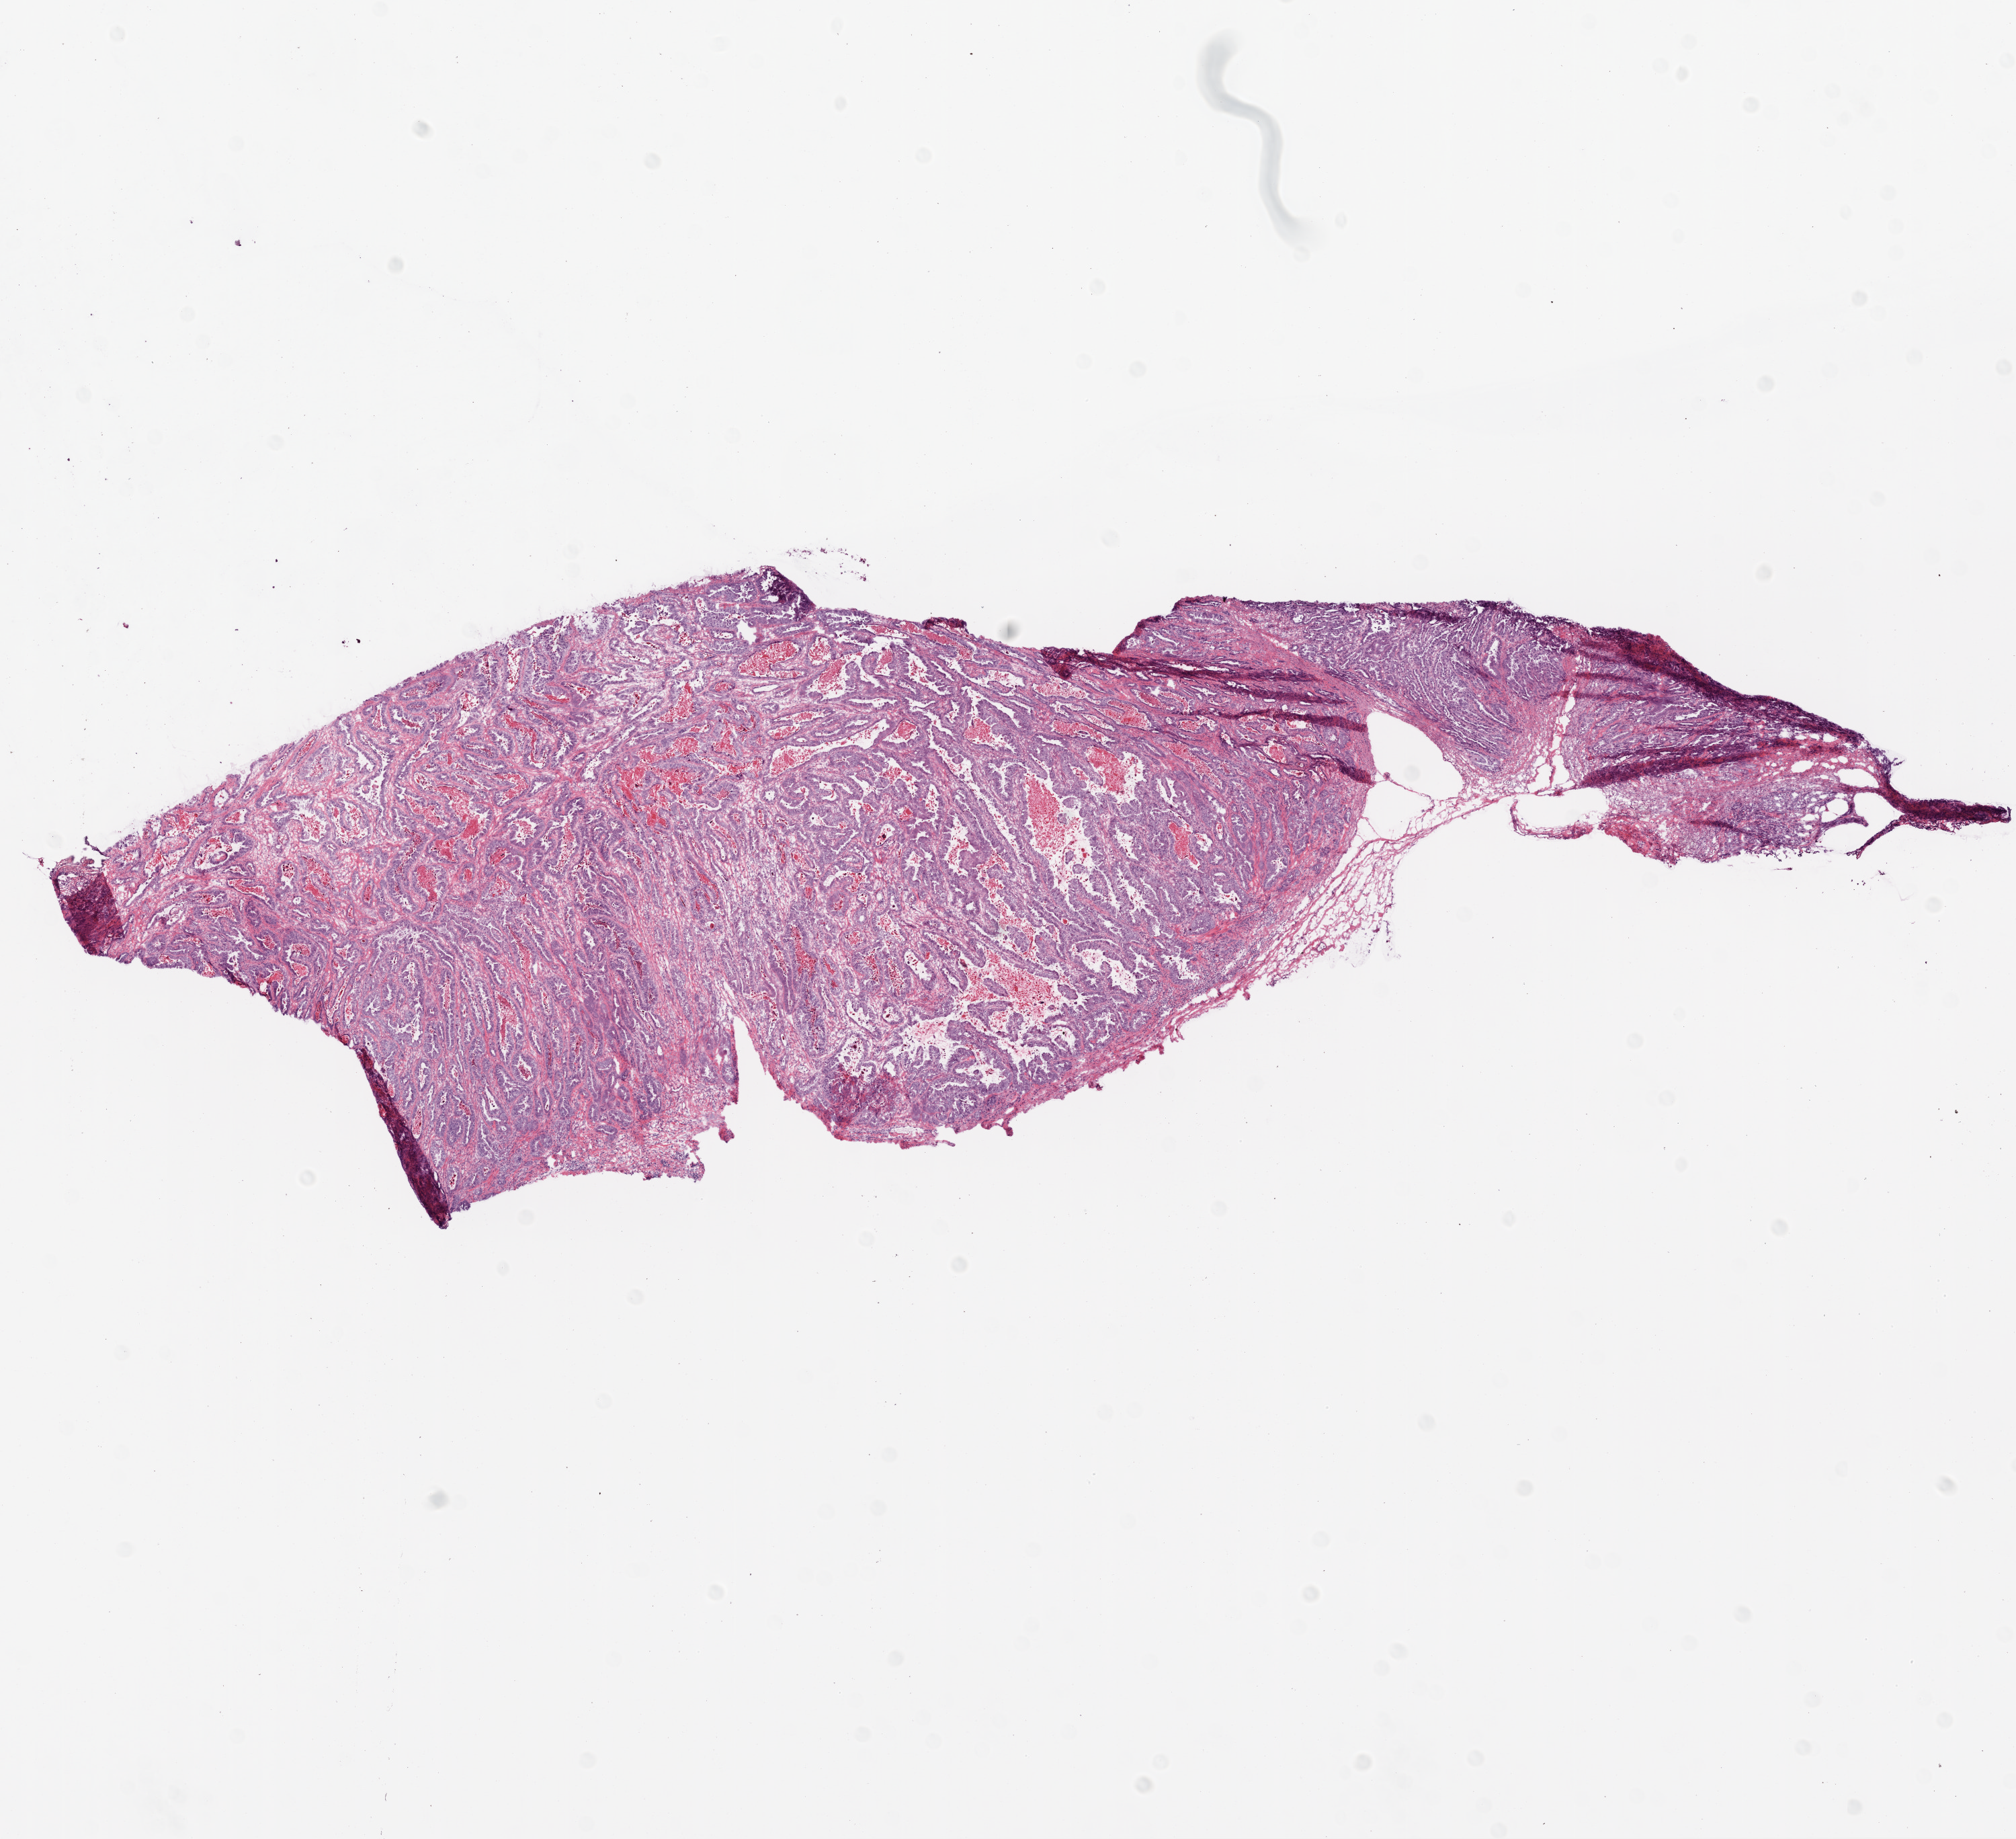
H&E-stained whole-slide image — low-resolution overview of the scanned area, about 12.0 x 11.0 mm; frozen section from the top of the tissue portion; ovary, primary tumour sample. Patient: female, age at initial diagnosis 60 years. Histologic grade: G3 (poorly differentiated). Pathologist review of this section (percent, as recorded): tumour cells 80%, tumour nuclei 80%, normal cells 0%, stromal cells 20%, necrosis 0%.
Pathologic diagnosis: Serous cystadenocarcinoma, NOS. FIGO stage: IIIC.